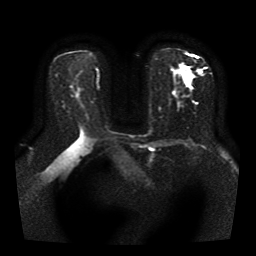
Breast MRI, one axial slice. Slice 22 of 41 in the series (ordered by position). Diffusion-weighted series; image 2 of 4 stored at this slice position (different b-values; order by instance number). 1.5 T. 5 mm slice thickness. 256 × 256 image matrix, field of view 330 × 330 mm. Female patient.
Annotated regions visible in this slice (manually delineated by an expert):
- tumour on diffusion-weighted imaging: bounding box <197,69,201,73> (left, top, right, bottom; pixels)